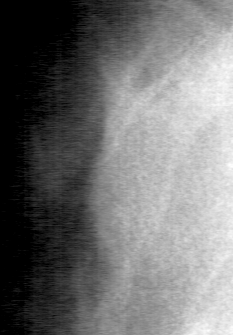
Region of interest cut from a scanned film mammogram (one marked finding); left breast; CC view; BI-RADS breast density category 1 (scale 1–4).
Finding: mass, shape irregular, margins ill defined; BI-RADS assessment category 2; subtlety rating 2 on a 1 (subtle) to 5 (obvious) scale; pathology (as recorded): benign.